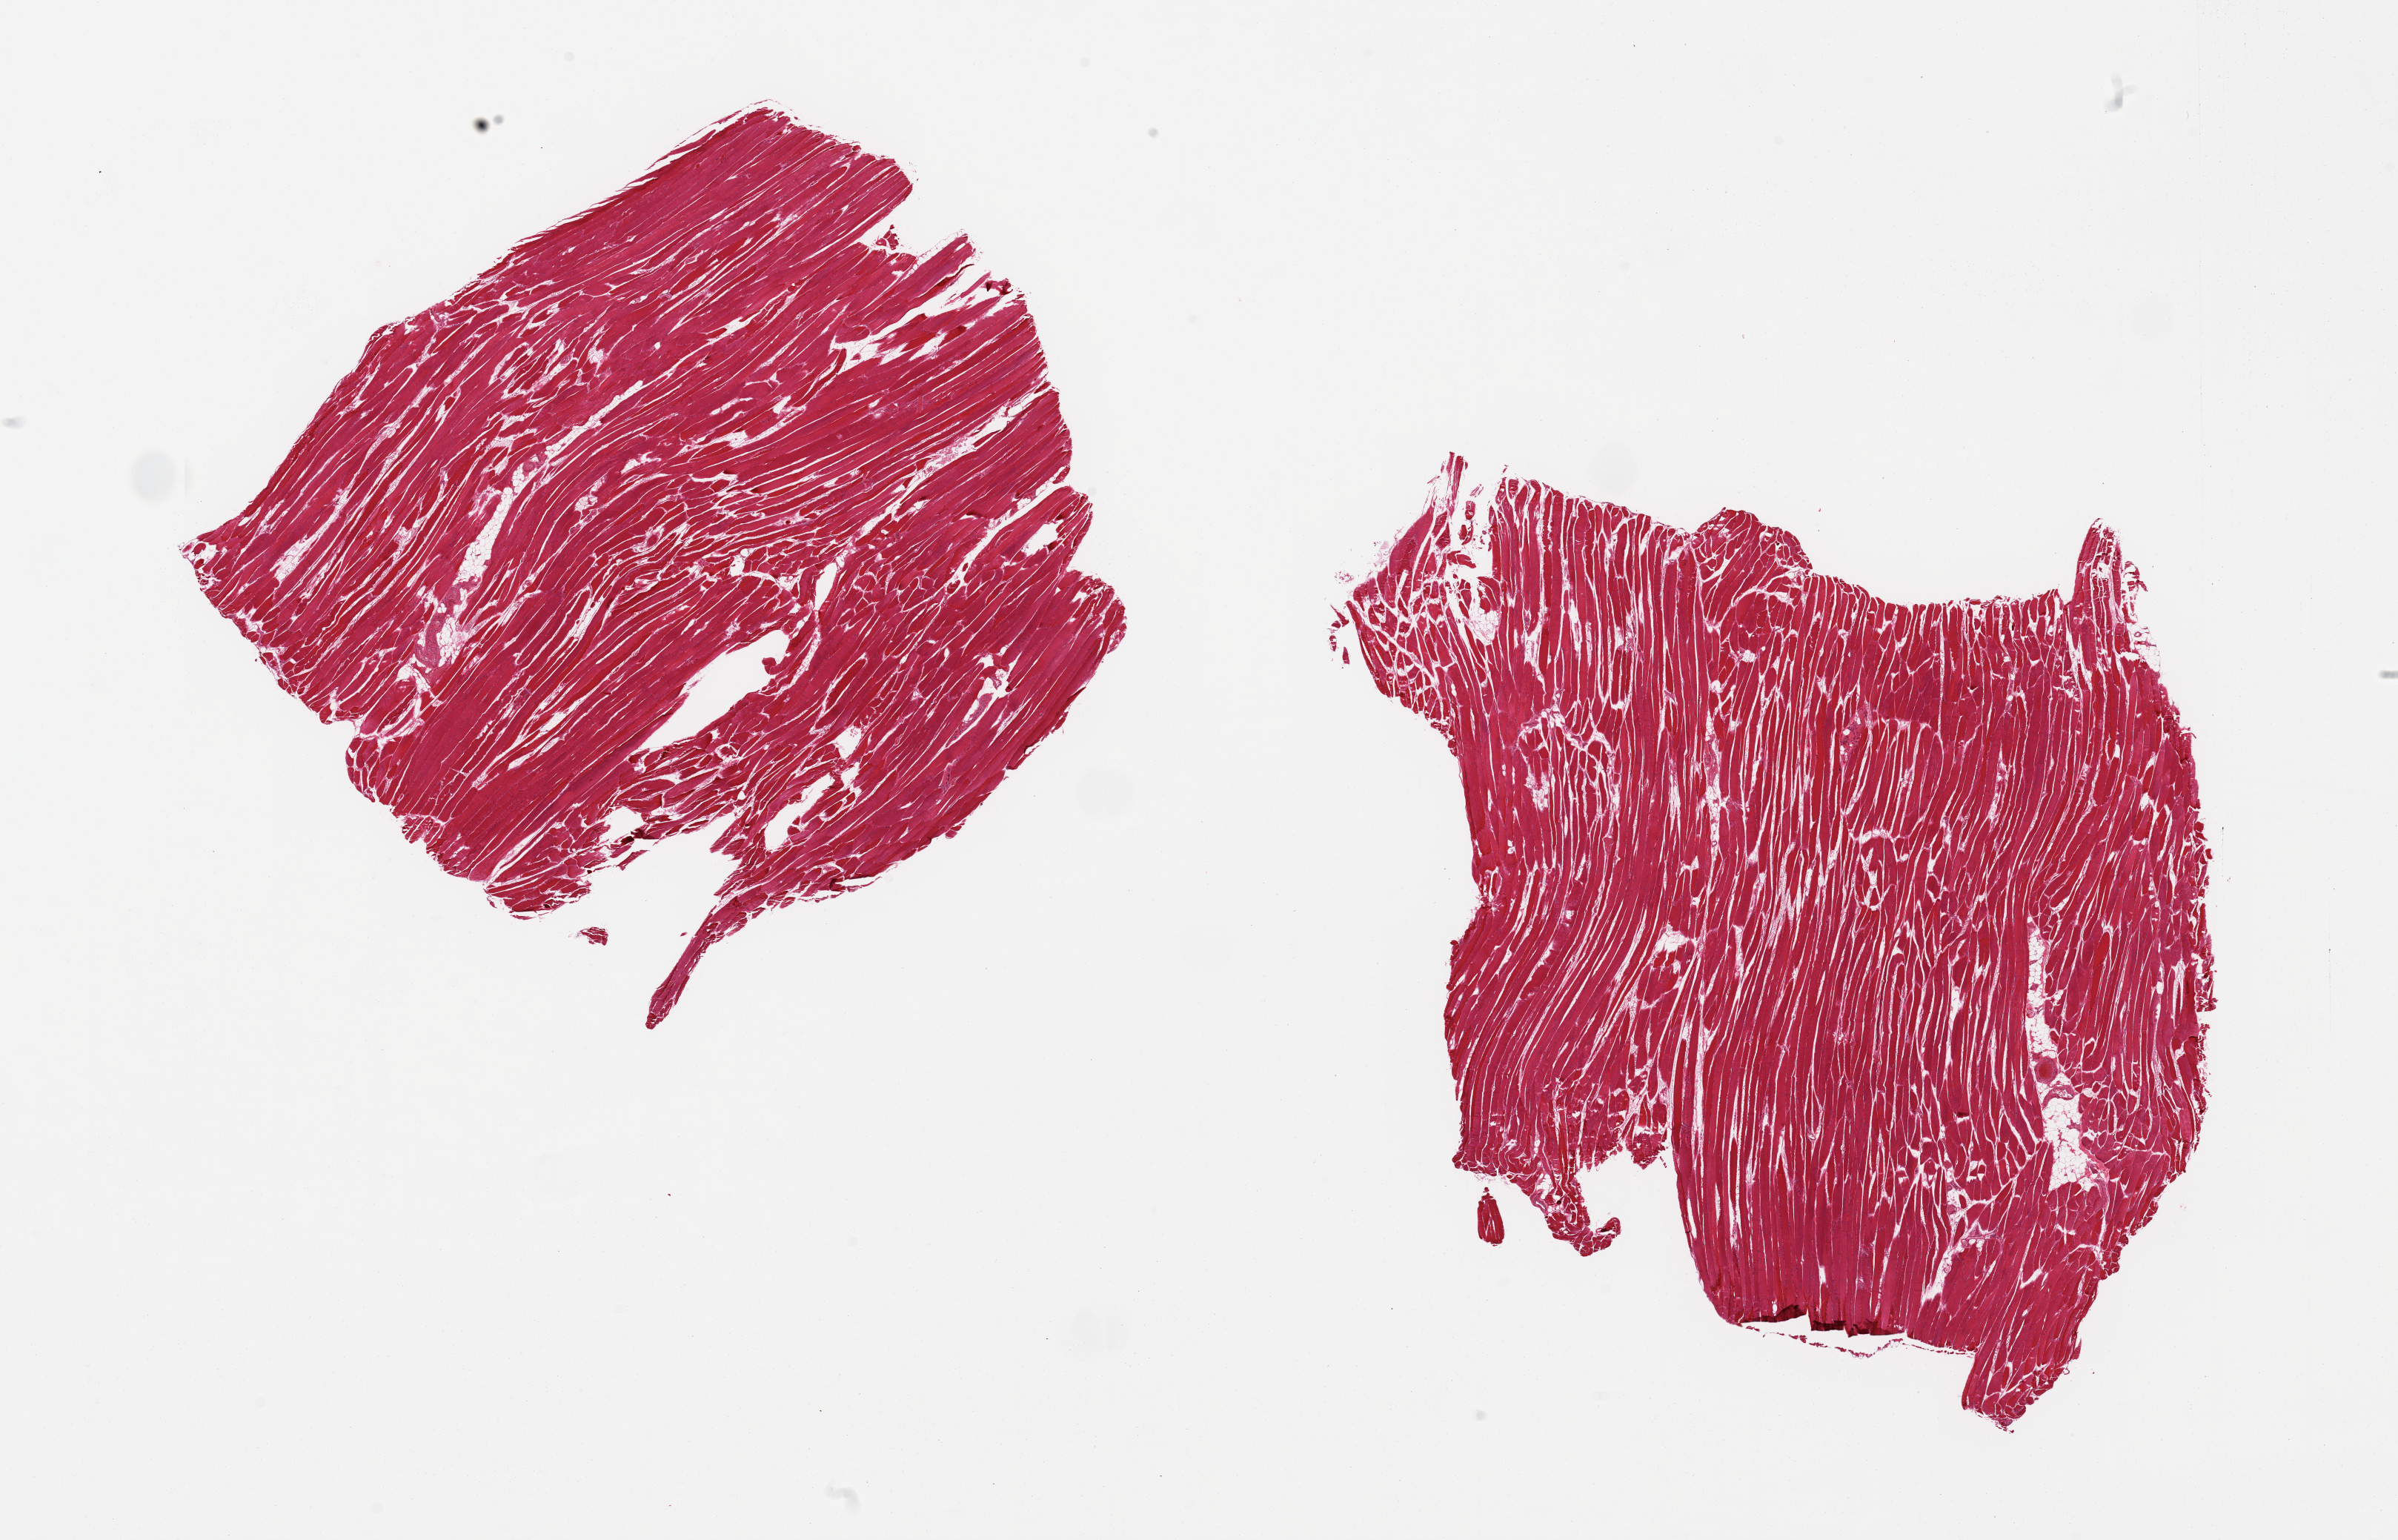
H&E whole-slide image, low-resolution overview of the scanned area, about 25.6 x 16.4 mm (slide scanned at 20x). PAXgene-fixed paraffin-embedded (PFPE) section. Sampled site (target tissue): skeletal muscle. Tissue donor sample.
Reviewer comment on this tissue sample: 2 pieces; <5% internal fat.